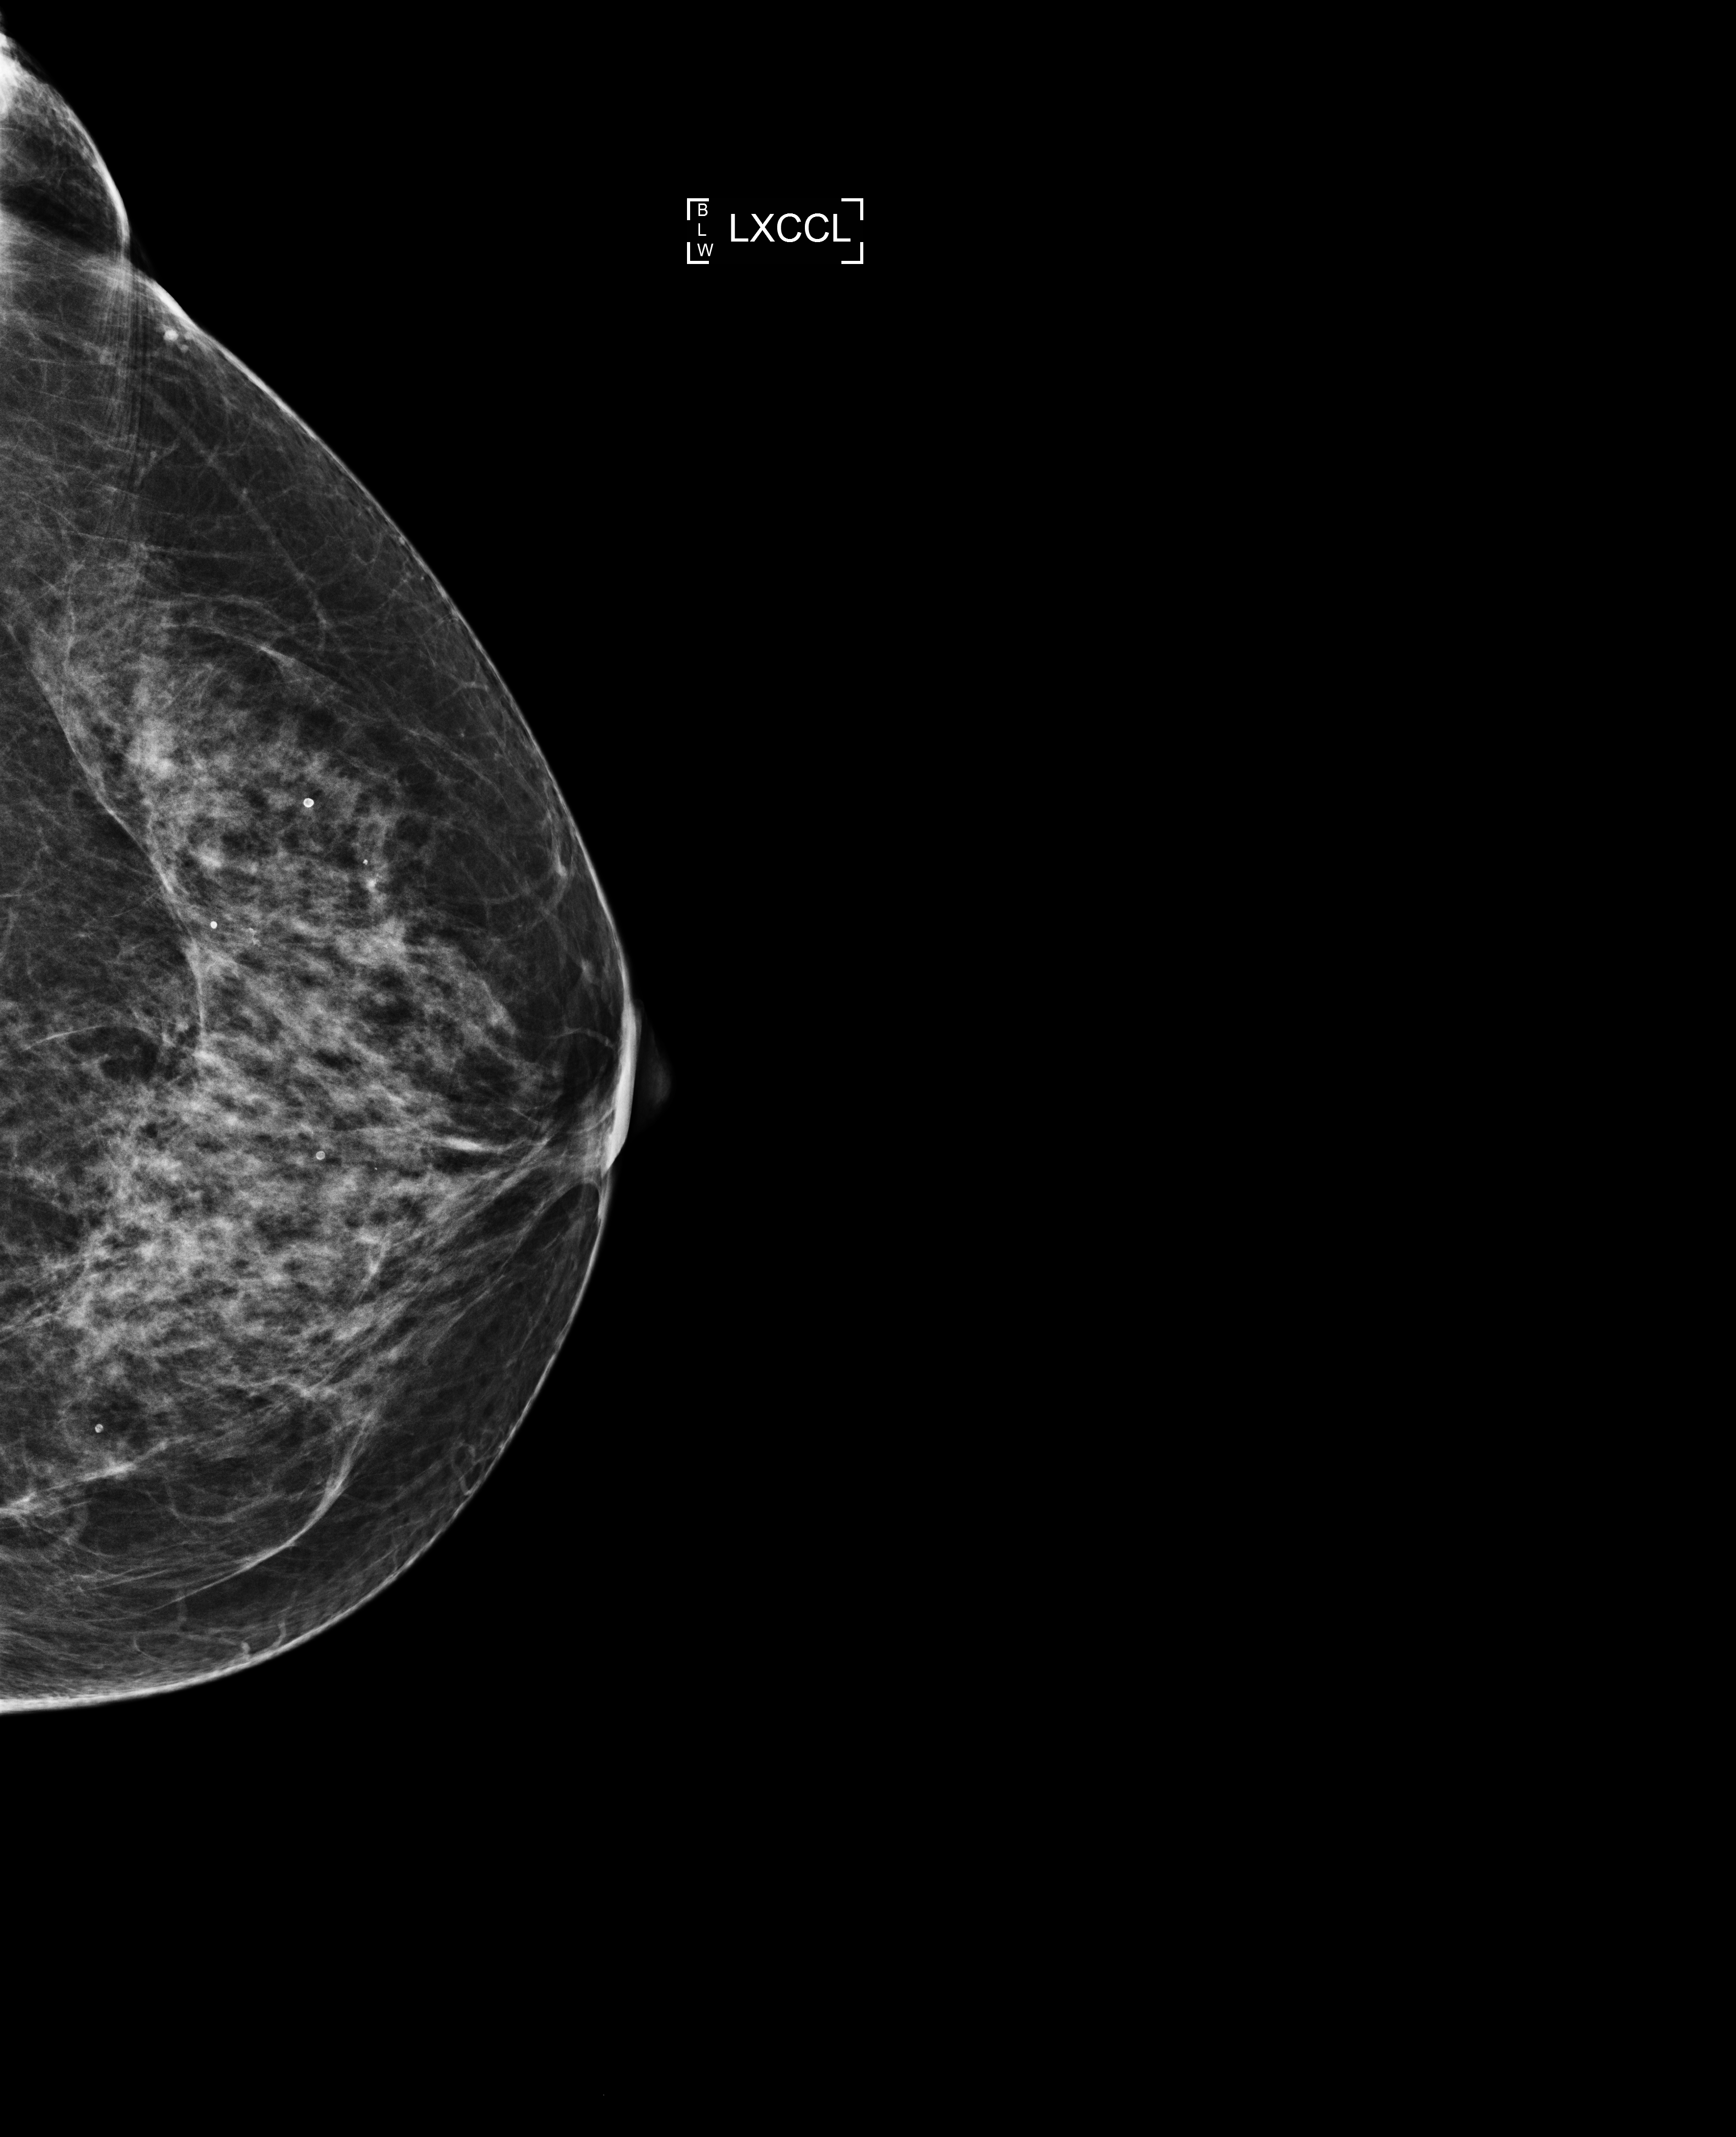
Annual screening mammography examination; system: Selenia Dimensions. Patient aged 60 years (female).
Image type: full-field digital mammogram. Breast: left. Projection: exaggerated CC view (lateral).